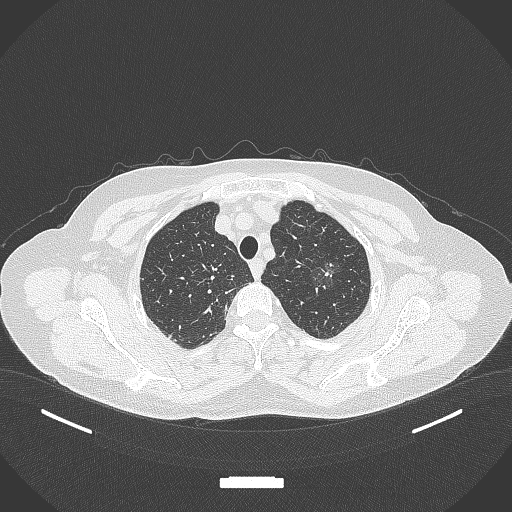
Chest CT, one axial slice. Position 302 of 369 along the scan axis. Lung window (W 1500 / L -600 HU). 1 mm slice thickness. 512 × 512 image matrix, field of view 400 × 400 mm. Female patient, age 64 years. From the clinical record (not read from this slice): clinical TNM (as recorded): T1c N0 M0.
Annotated regions visible in this slice (bounding box drawn by a radiologist):
- lung tumour (recorded histology: adenocarcinoma): bounding box (x1, y1, x2, y2) in pixels: (310, 253, 339, 292)